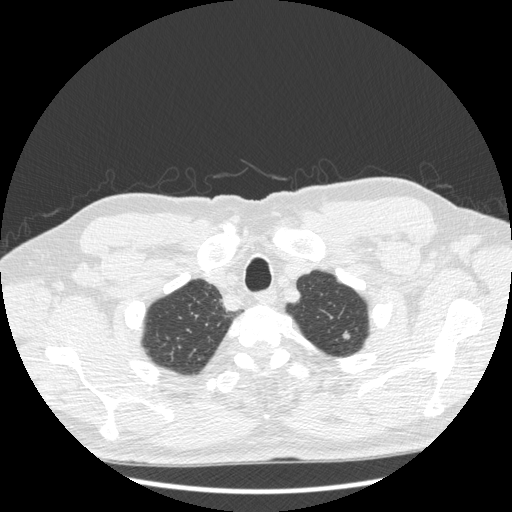
Low-dose screening chest CT, one axial slice. Slice 196 of 223 in the series (ordered by position). Lung window (W 1500 / L -600 HU). 512 × 512 image matrix, field of view 380 × 380 mm.
Structures marked on this image (outlined manually by an expert reader):
- lesion 1 (tumor, upper lobe of left lung): box from (x=343, y=331) to (x=350, y=339) px